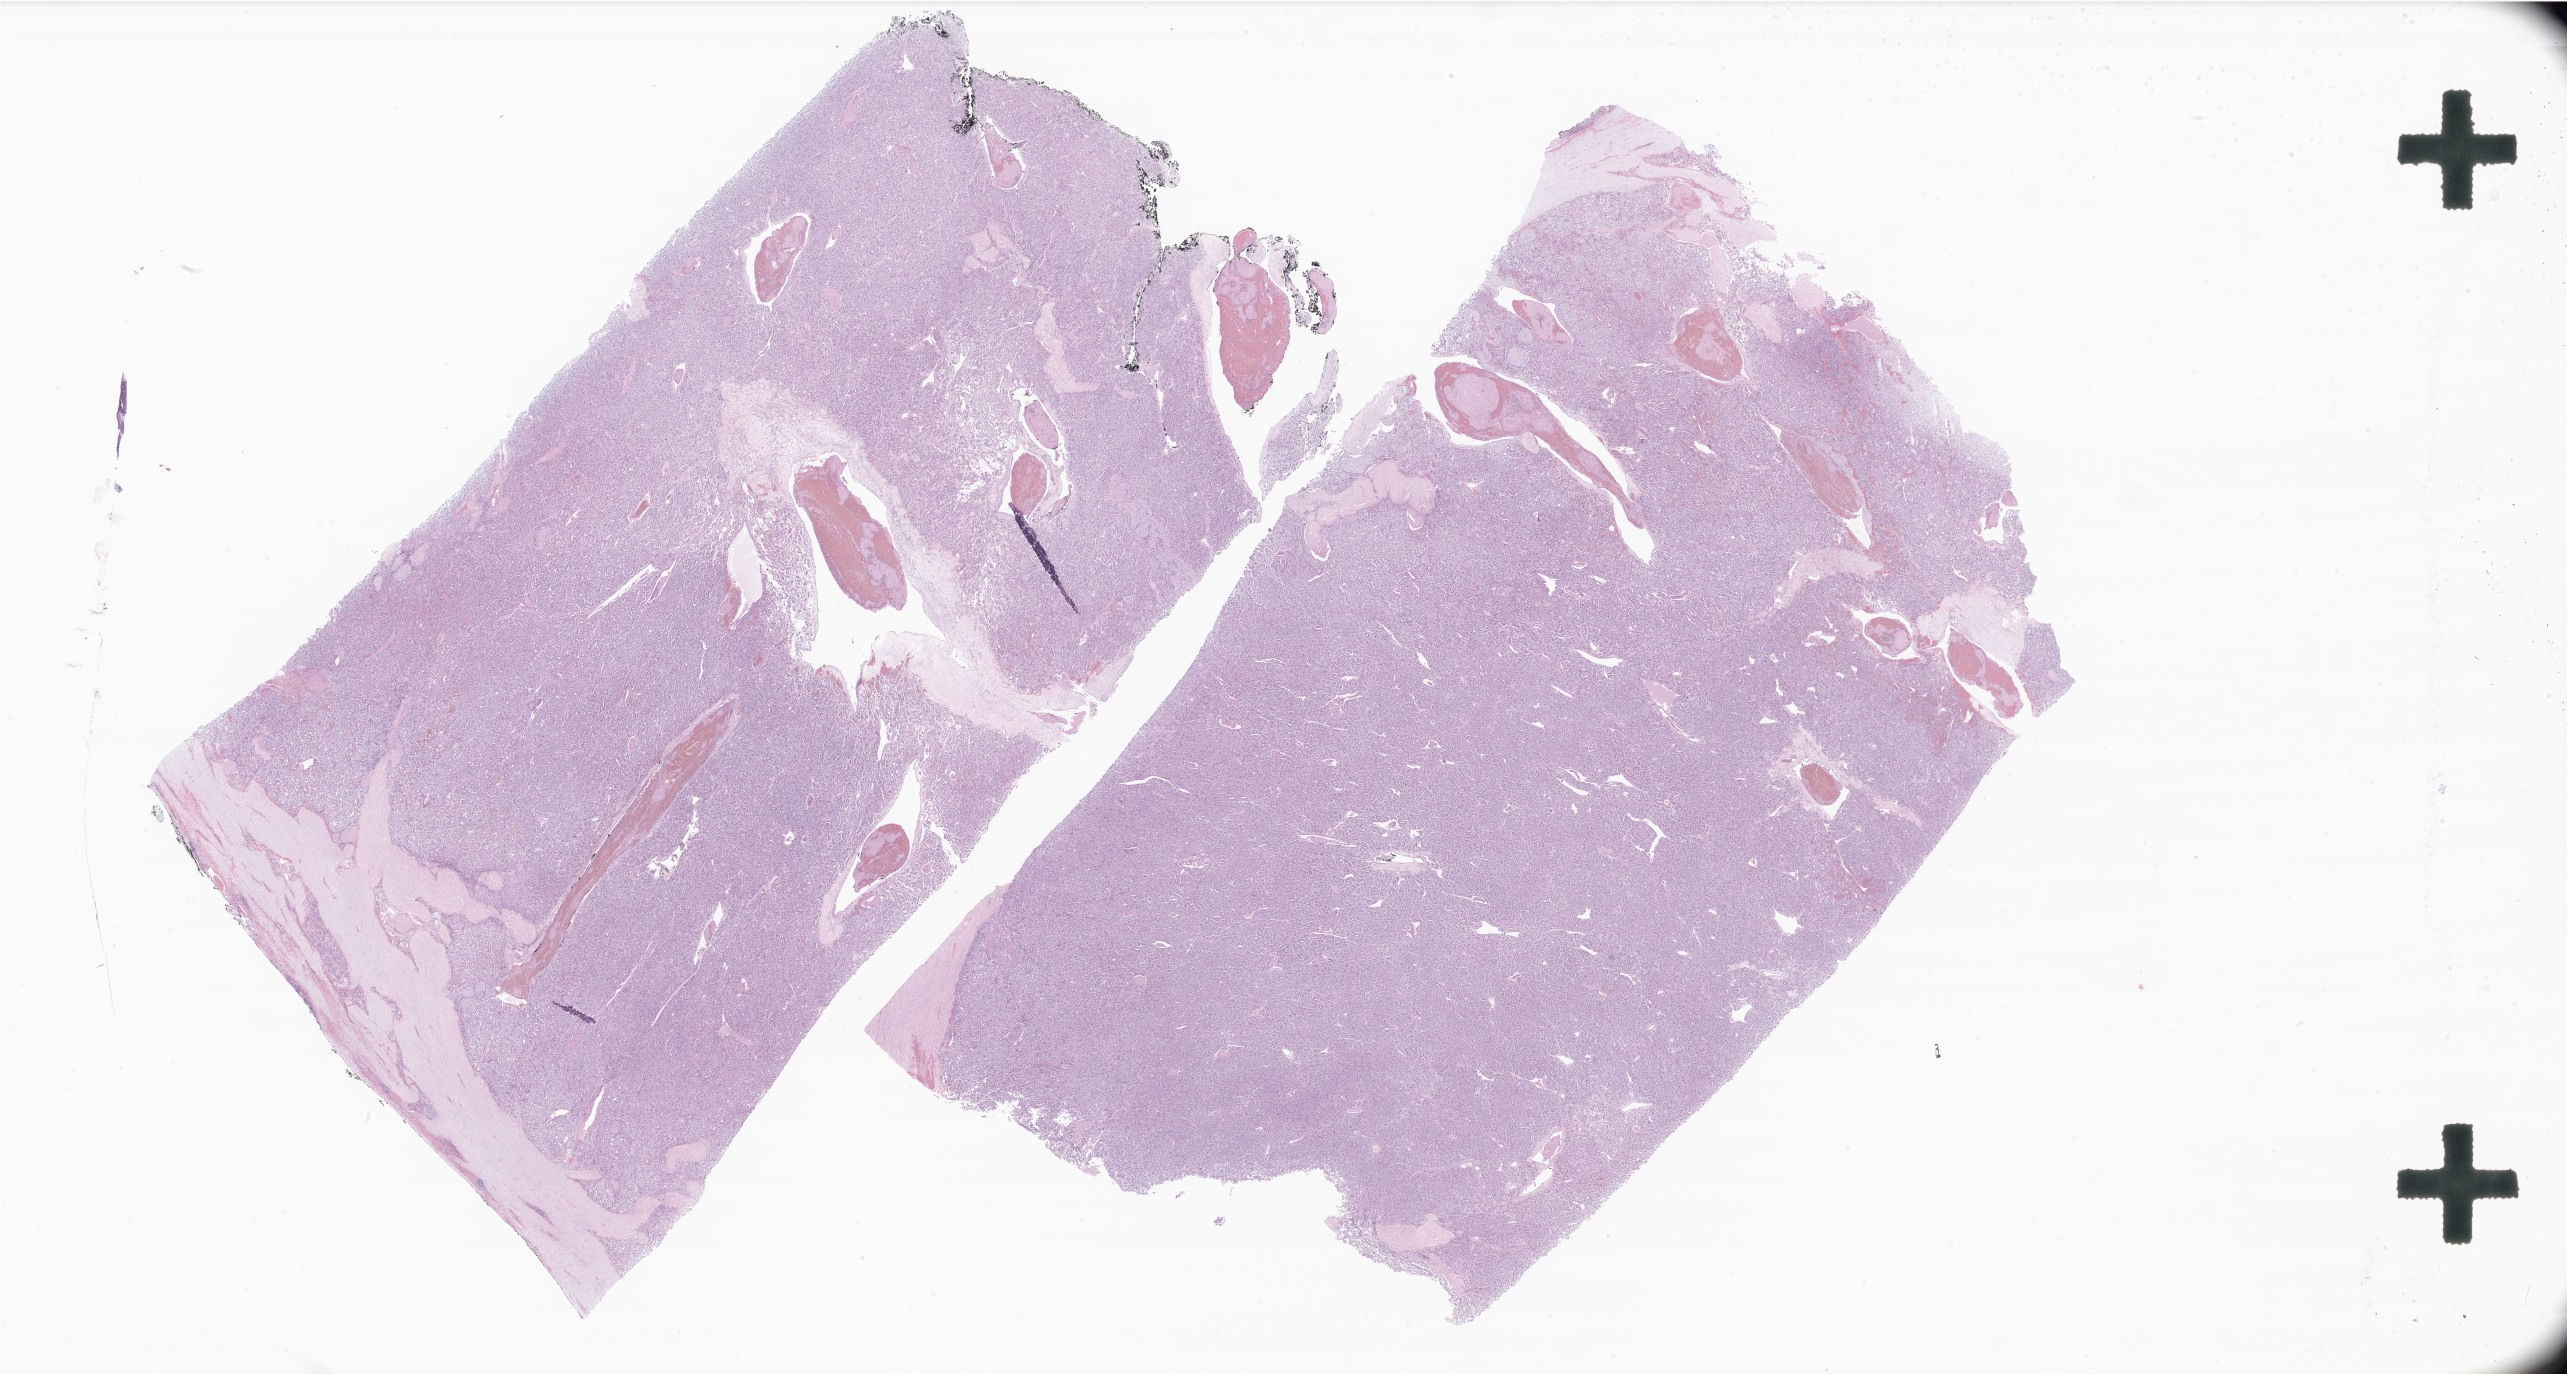
Whole-slide image, H&E stain of tumor tissue from the retroperitoneum — whole scanned area (about 43.3 x 23.2 mm) shown as a low-resolution overview. Formalin-fixed, paraffin-embedded (FFPE) tissue. Patient: male, age 158 months (13 years 2 months).
• diagnosis (ICD-O-3 morphology term): Paraganglioma, NOS